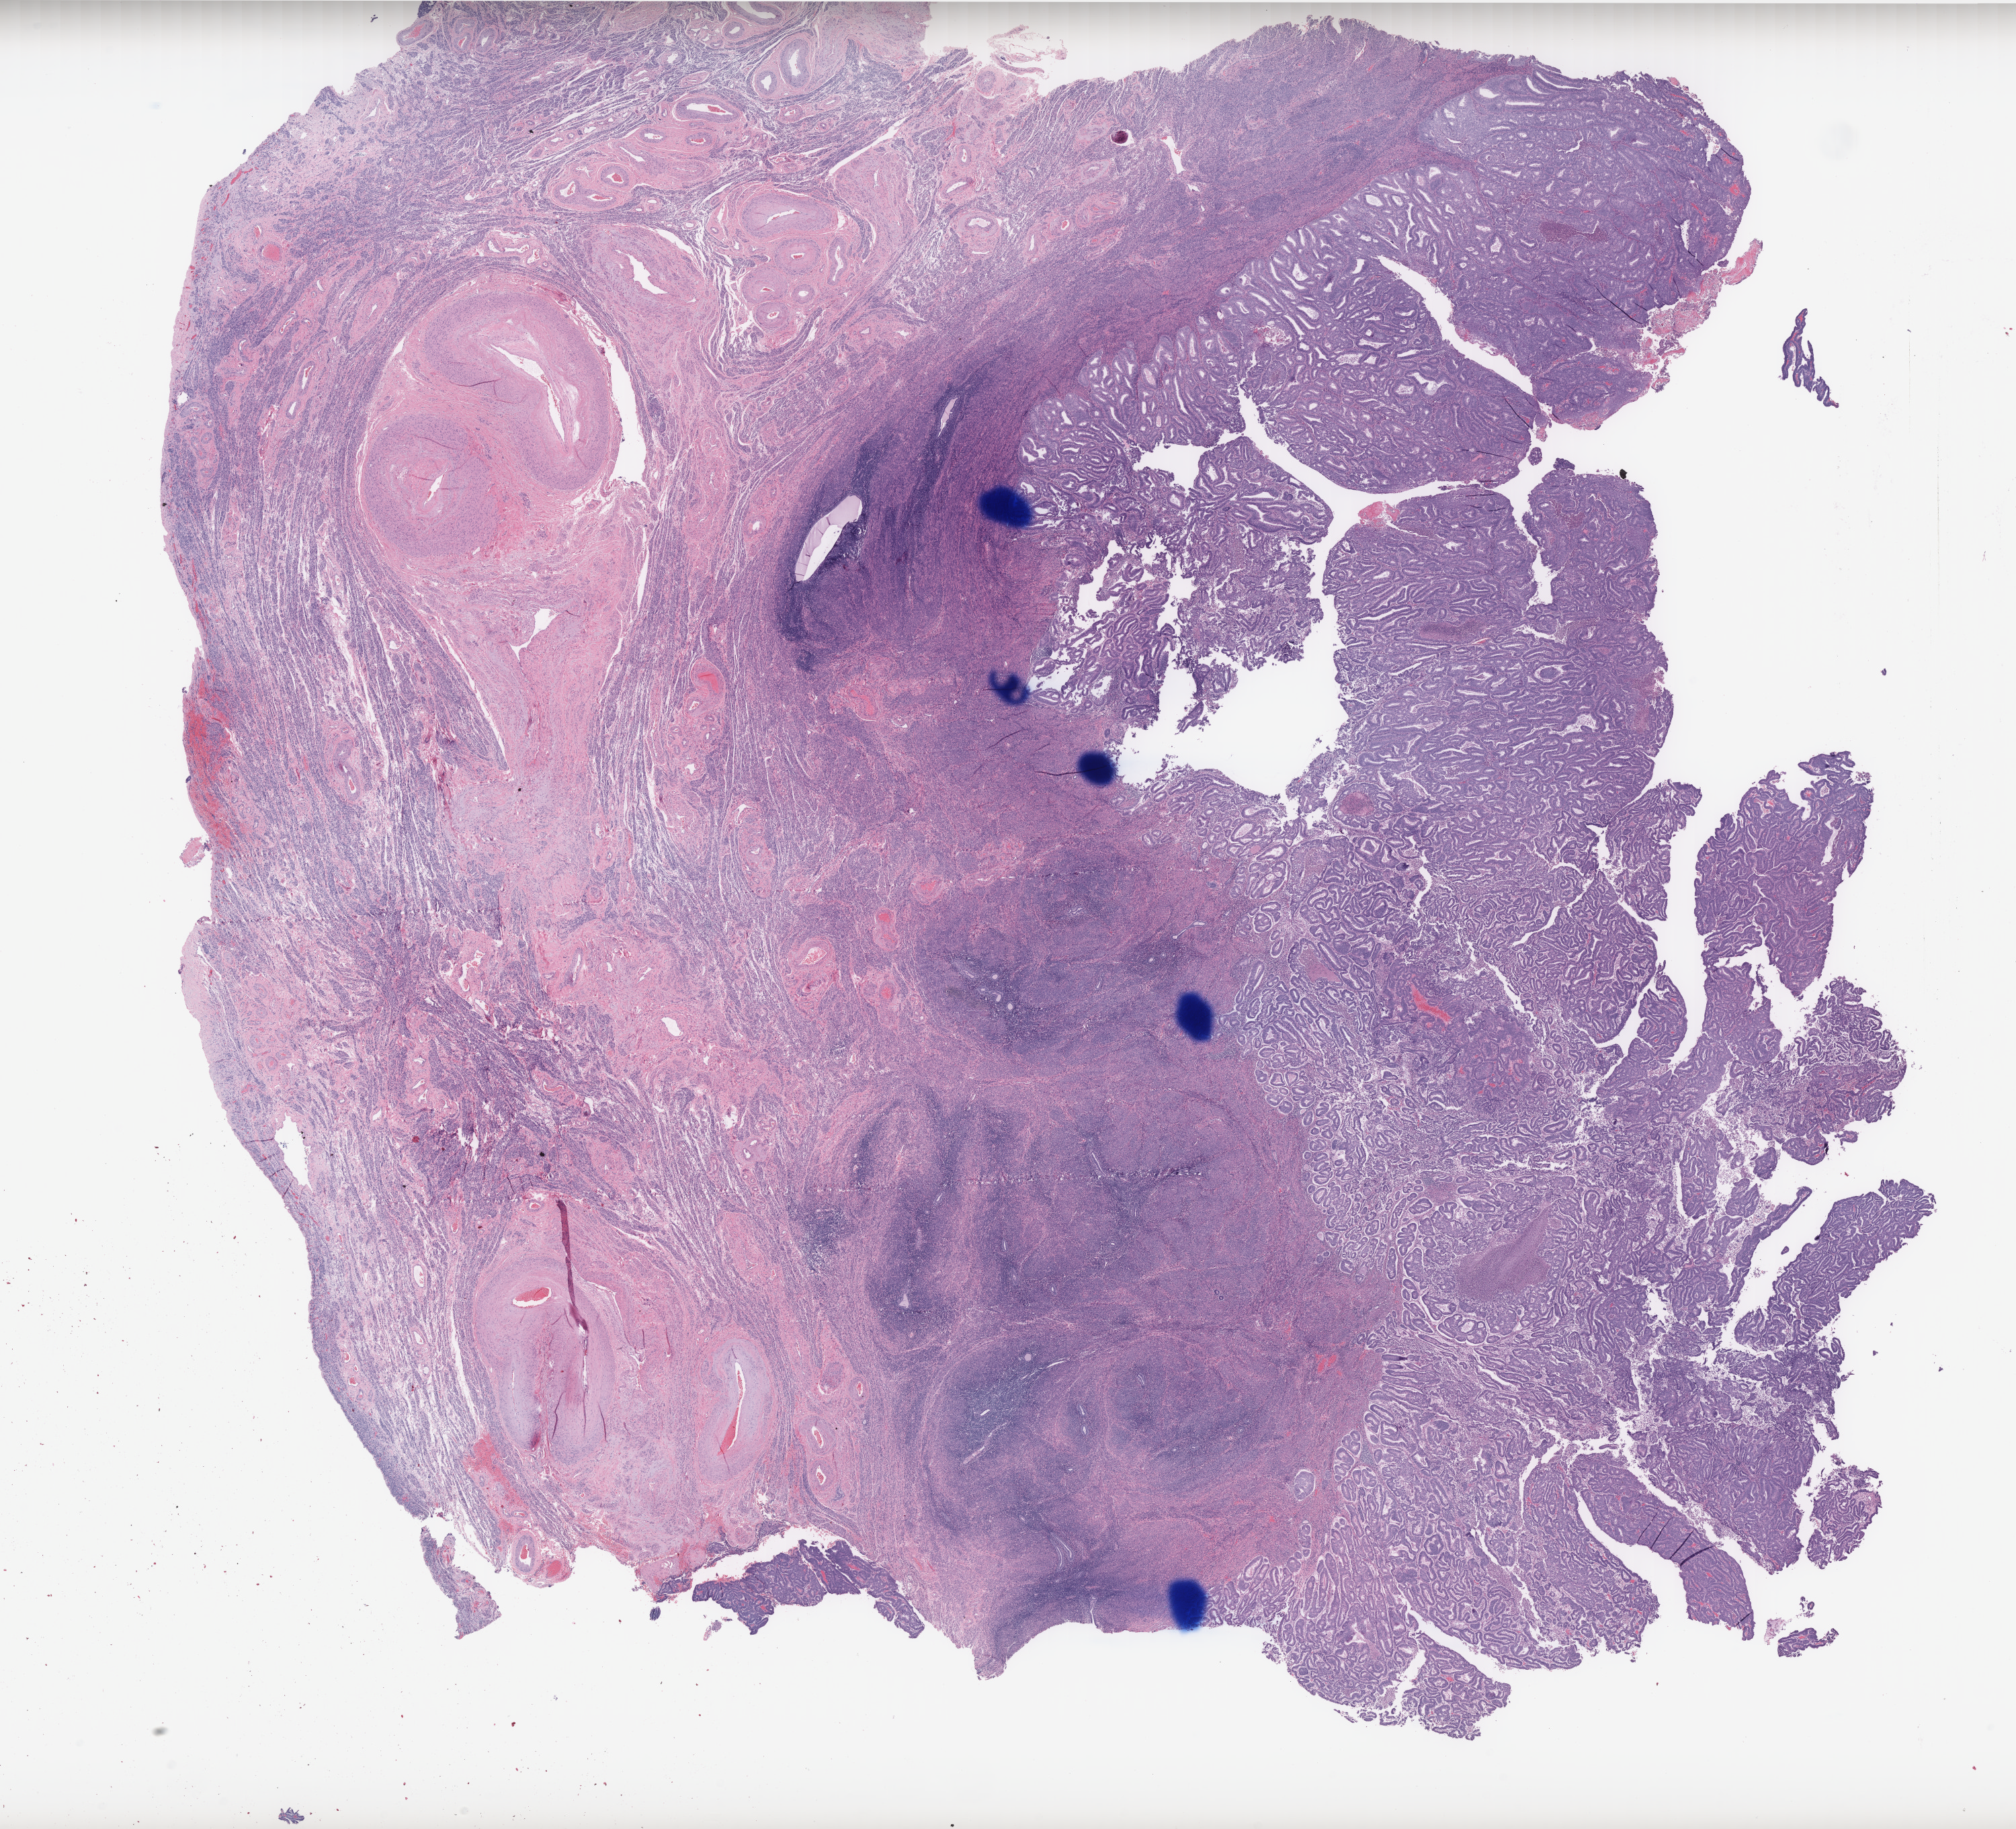
Digitized H&E-stained tissue section (whole slide), shown as a low-resolution overview of the whole scanned area (about 24.1 x 21.8 mm, acquisition: 40x scan); FFPE section; sample: primary tumour, uterus. Female patient; age at initial diagnosis 73 years. Histologic grade: G1 (well differentiated).
Pathologic diagnosis: Endometrioid adenocarcinoma, NOS. FIGO stage: IA. Lymph nodes positive (case pathology): 0 of 2 examined.